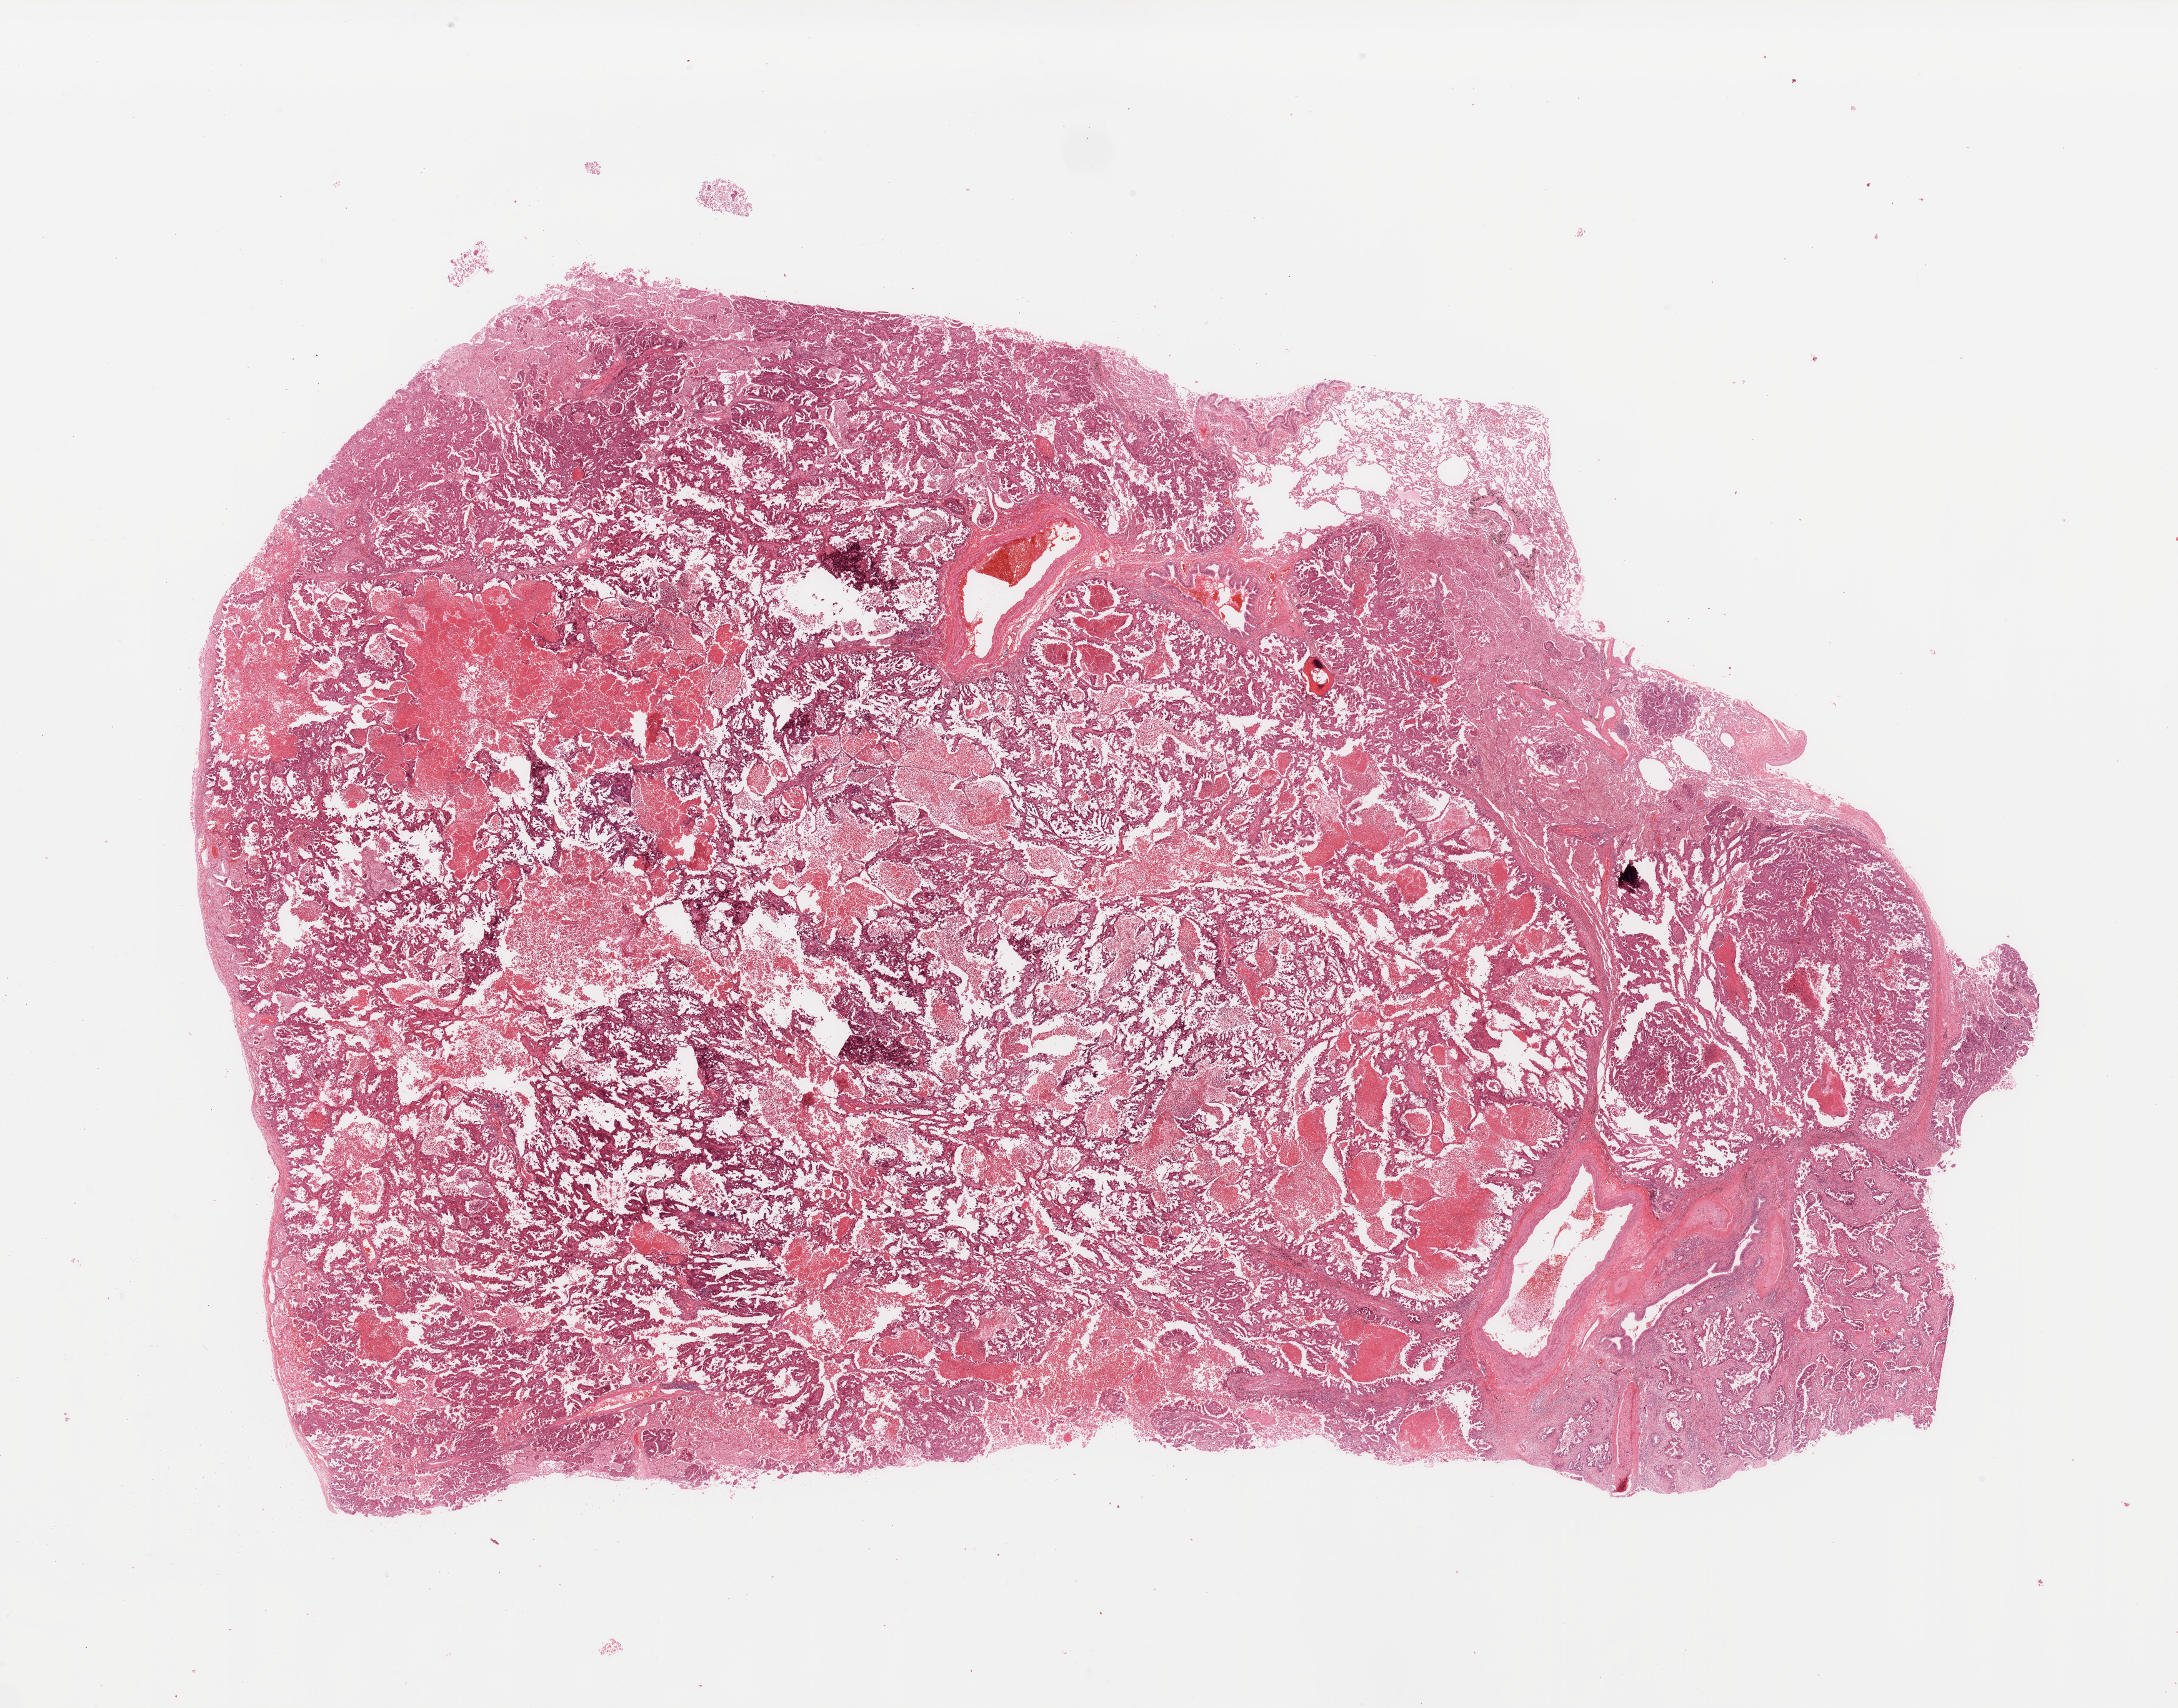
Digitized H&E-stained tissue section (whole slide), shown as a low-resolution overview of the whole scanned area (about 27.6 x 21.6 mm, slide scanned at 20x), tumour tissue sample, lung. Patient: female, age 66 years. Histologic grade: G3 (poorly differentiated).
- histologic diagnosis: Adenocarcinoma, NOS
- AJCC pathologic stage: IIB